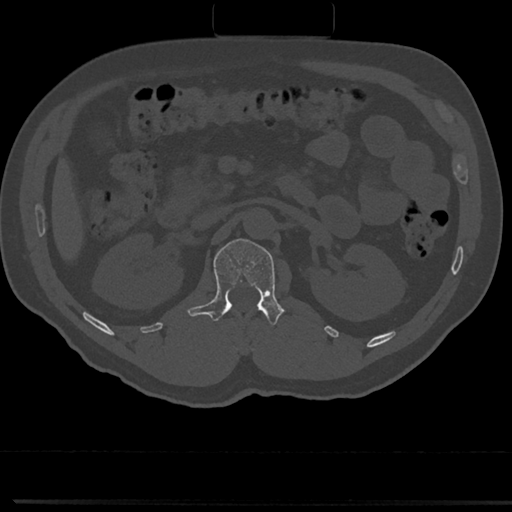
CT including the spine, one axial slice. Position 89 of 817 along the scan axis. 120 kVp. Bone window (W 1800 / L 400 HU). 0.5 mm slice thickness. 512 × 512 image matrix, field of view 355 × 355 mm. Male patient, age 61 years. Case-level facts recorded for this patient, not image findings: primary cancer: prostate.
Annotated regions visible in this slice (semi-automatic segmentation, software-assisted and operator-edited):
- L1 vertebra: box from (x=191, y=239) to (x=284, y=326) px